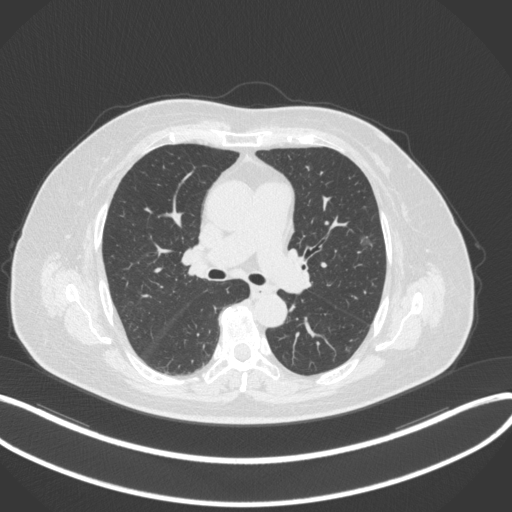
Chest CT, one axial slice; lung window (W 1500 / L -600 HU); 1 mm slice thickness; 512 × 512 image matrix. Patient: female, 76 years. Case-level facts recorded for this patient, not image findings: clinical TNM (as recorded): T1b N0 M0; histopathological grade: G1-2.
Annotated regions visible in this slice (bounding box drawn by a radiologist):
- lung tumour (recorded histology: adenocarcinoma): bounding box (x1, y1, x2, y2) in pixels: (356, 230, 376, 255)